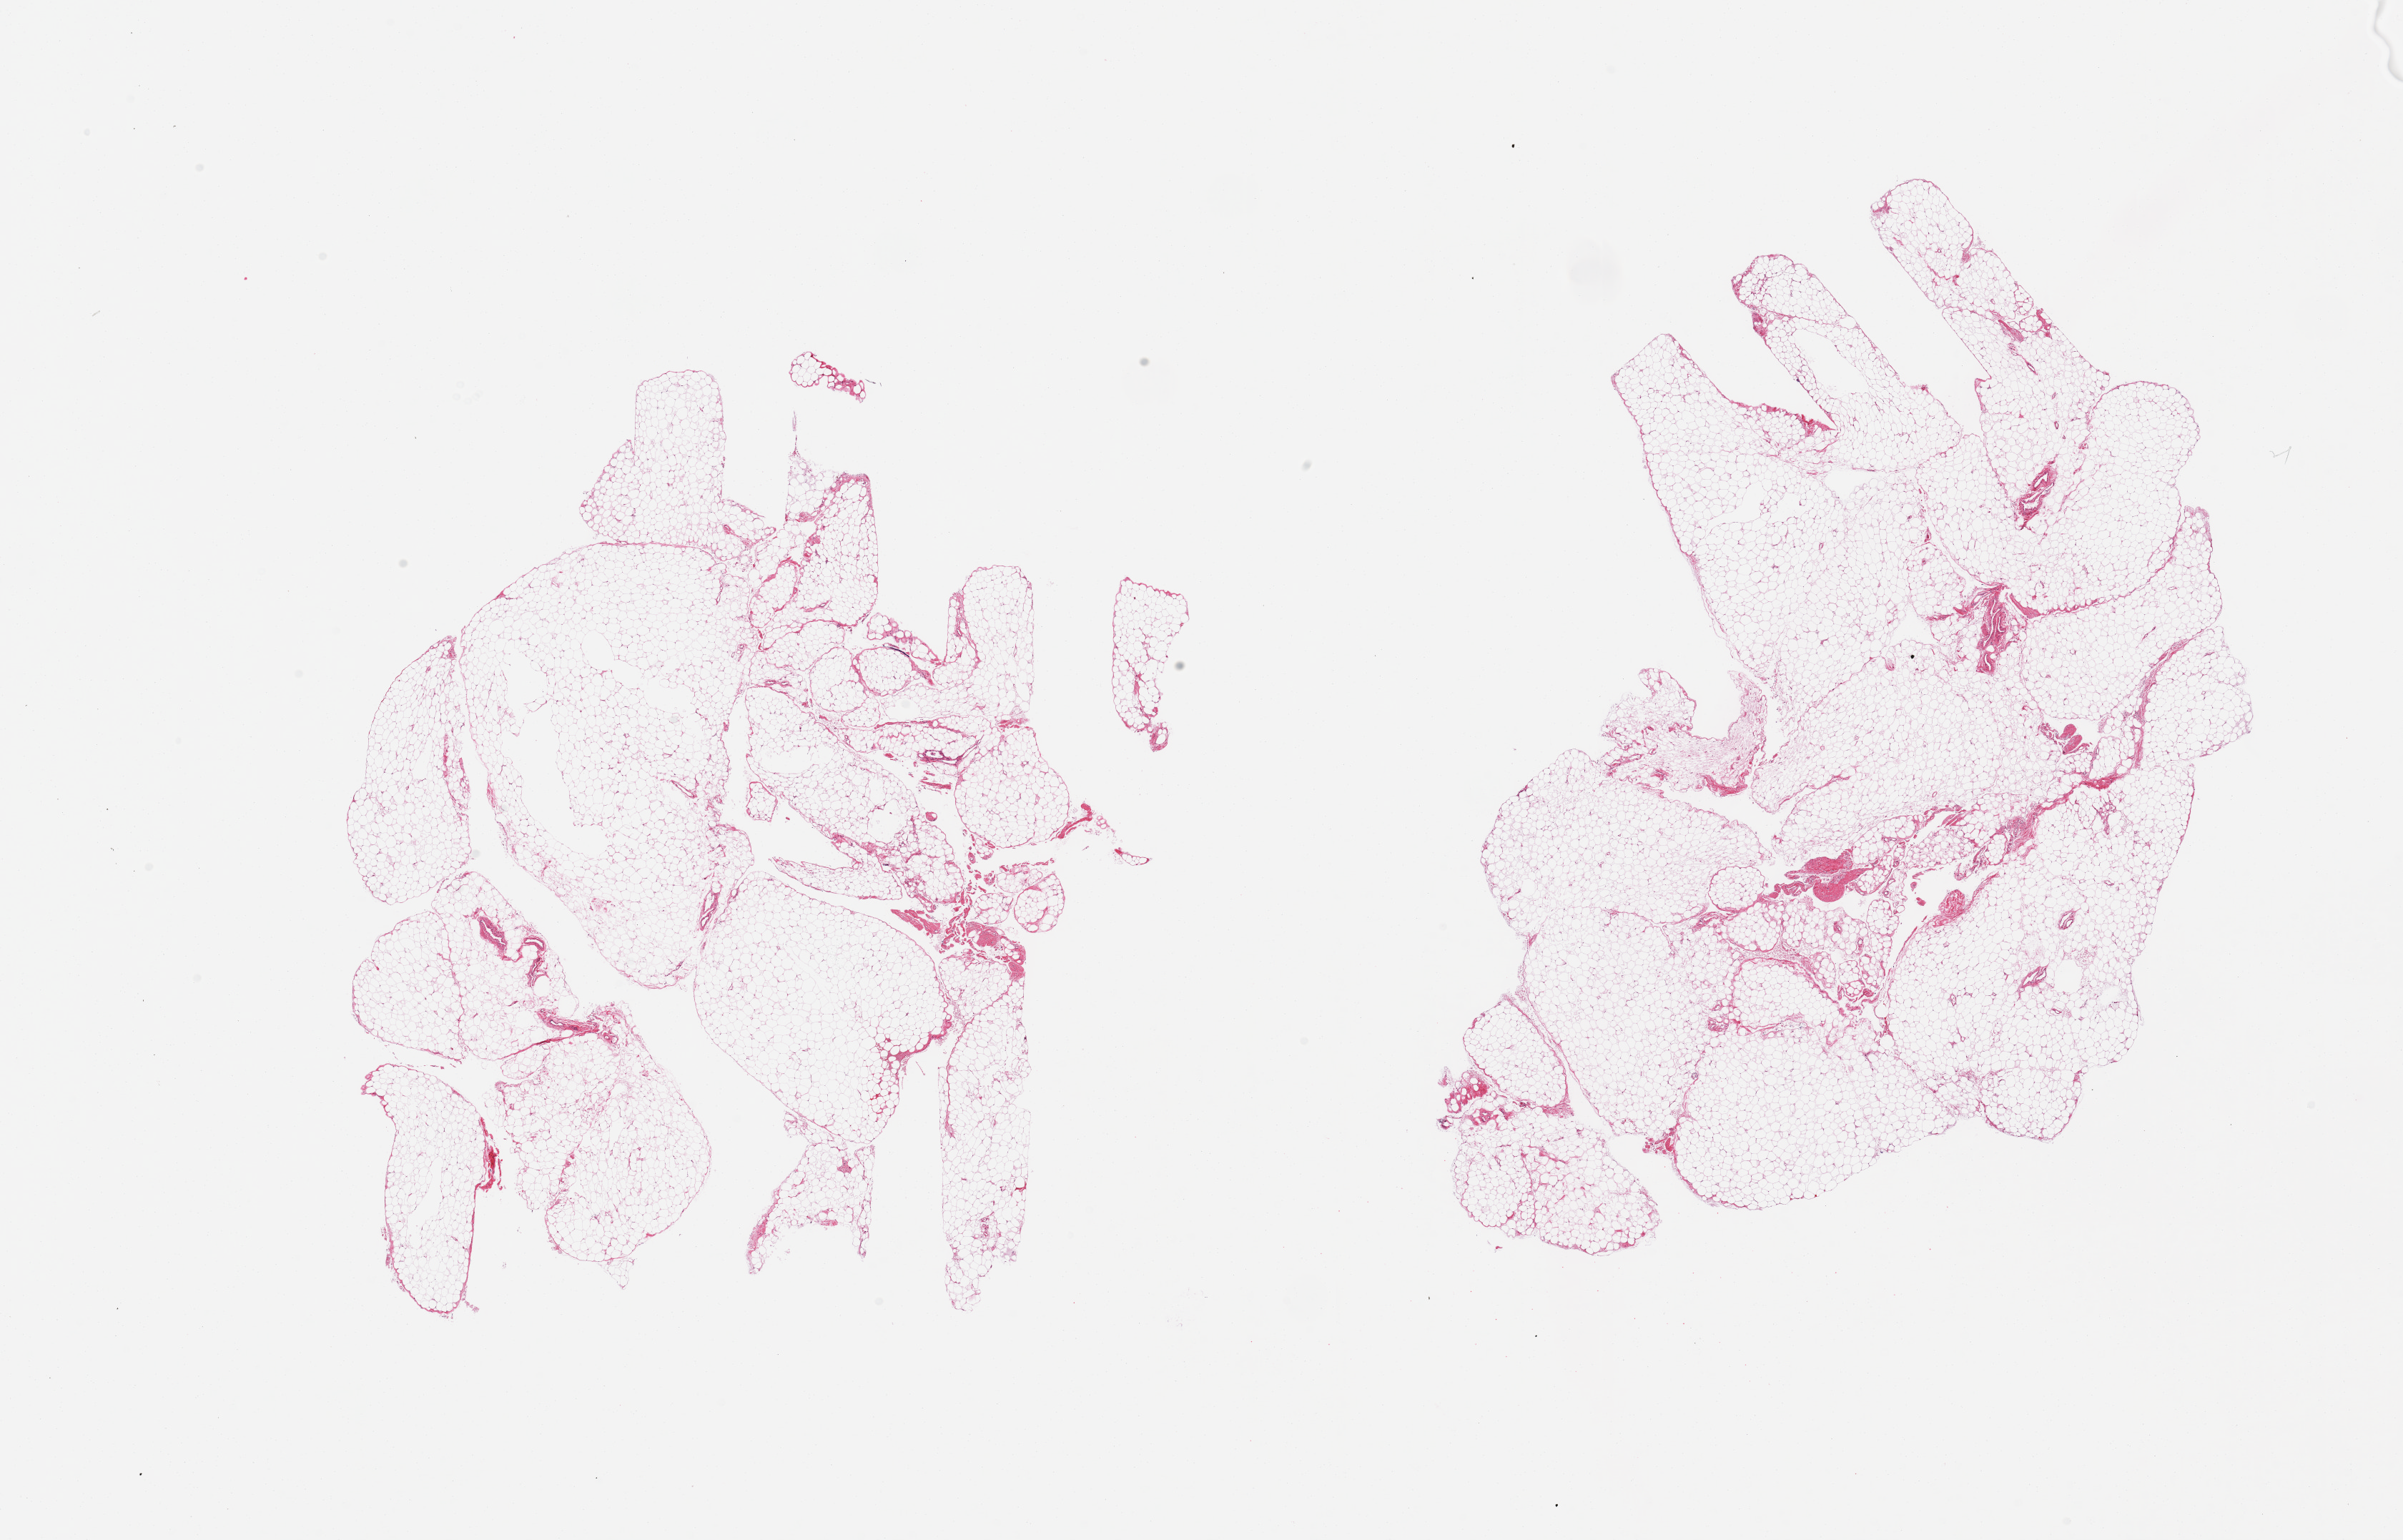
Haematoxylin and eosin whole-slide image — low-resolution overview of the scanned area, about 26.6 x 17.0 mm. PAXgene-fixed, paraffin-embedded tissue. Target tissue: omentum. Donor tissue sample. Male donor.
* review note (as recorded): 2 pieces, trace fascia/vascular elements